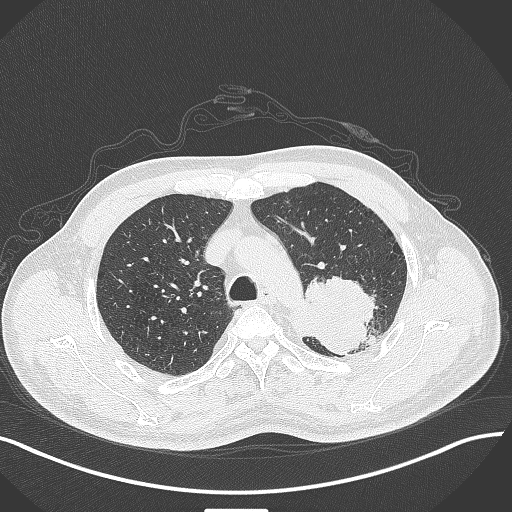
Chest CT, one axial slice. Slice 322 of 429 in the series (ordered by position). Reconstruction kernel B70f. Lung window (W 1500 / L -600 HU). 1 mm slice thickness. 512 × 512 image matrix, field of view 400 × 400 mm. Patient: male, 55 years. From the clinical record (not read from this slice): clinical TNM (as recorded): T3 N0 M1c; histopathological grade: G3.
Annotated regions visible in this slice (bounding box drawn by a radiologist):
- lung tumour (recorded histology: adenocarcinoma): box from (x=286, y=266) to (x=377, y=357) px